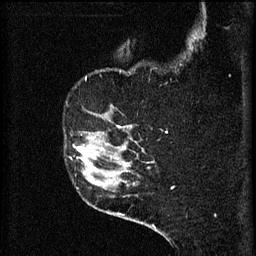
Breast MRI (dynamic contrast-enhanced), one sagittal slice. Position 46 of 60 along the scan axis. 3 images stored at this slice position (order not interpretable as contrast timing). 1.5 T. TE 4.2 ms, TR 8.2 ms. 256 × 256 image matrix. Female patient, age 49 years.
Structures marked on this image (semi-automatically segmented with operator editing):
- analysis volume of interest (the breast-tissue region the enhancement analysis was run in; not a lesion): box from (x=65, y=132) to (x=105, y=177) px
- tumour enhancement mask (voxels above the 70 % enhancement threshold inside the analysis volume of interest): (x=74, y=138)–(x=104, y=177)